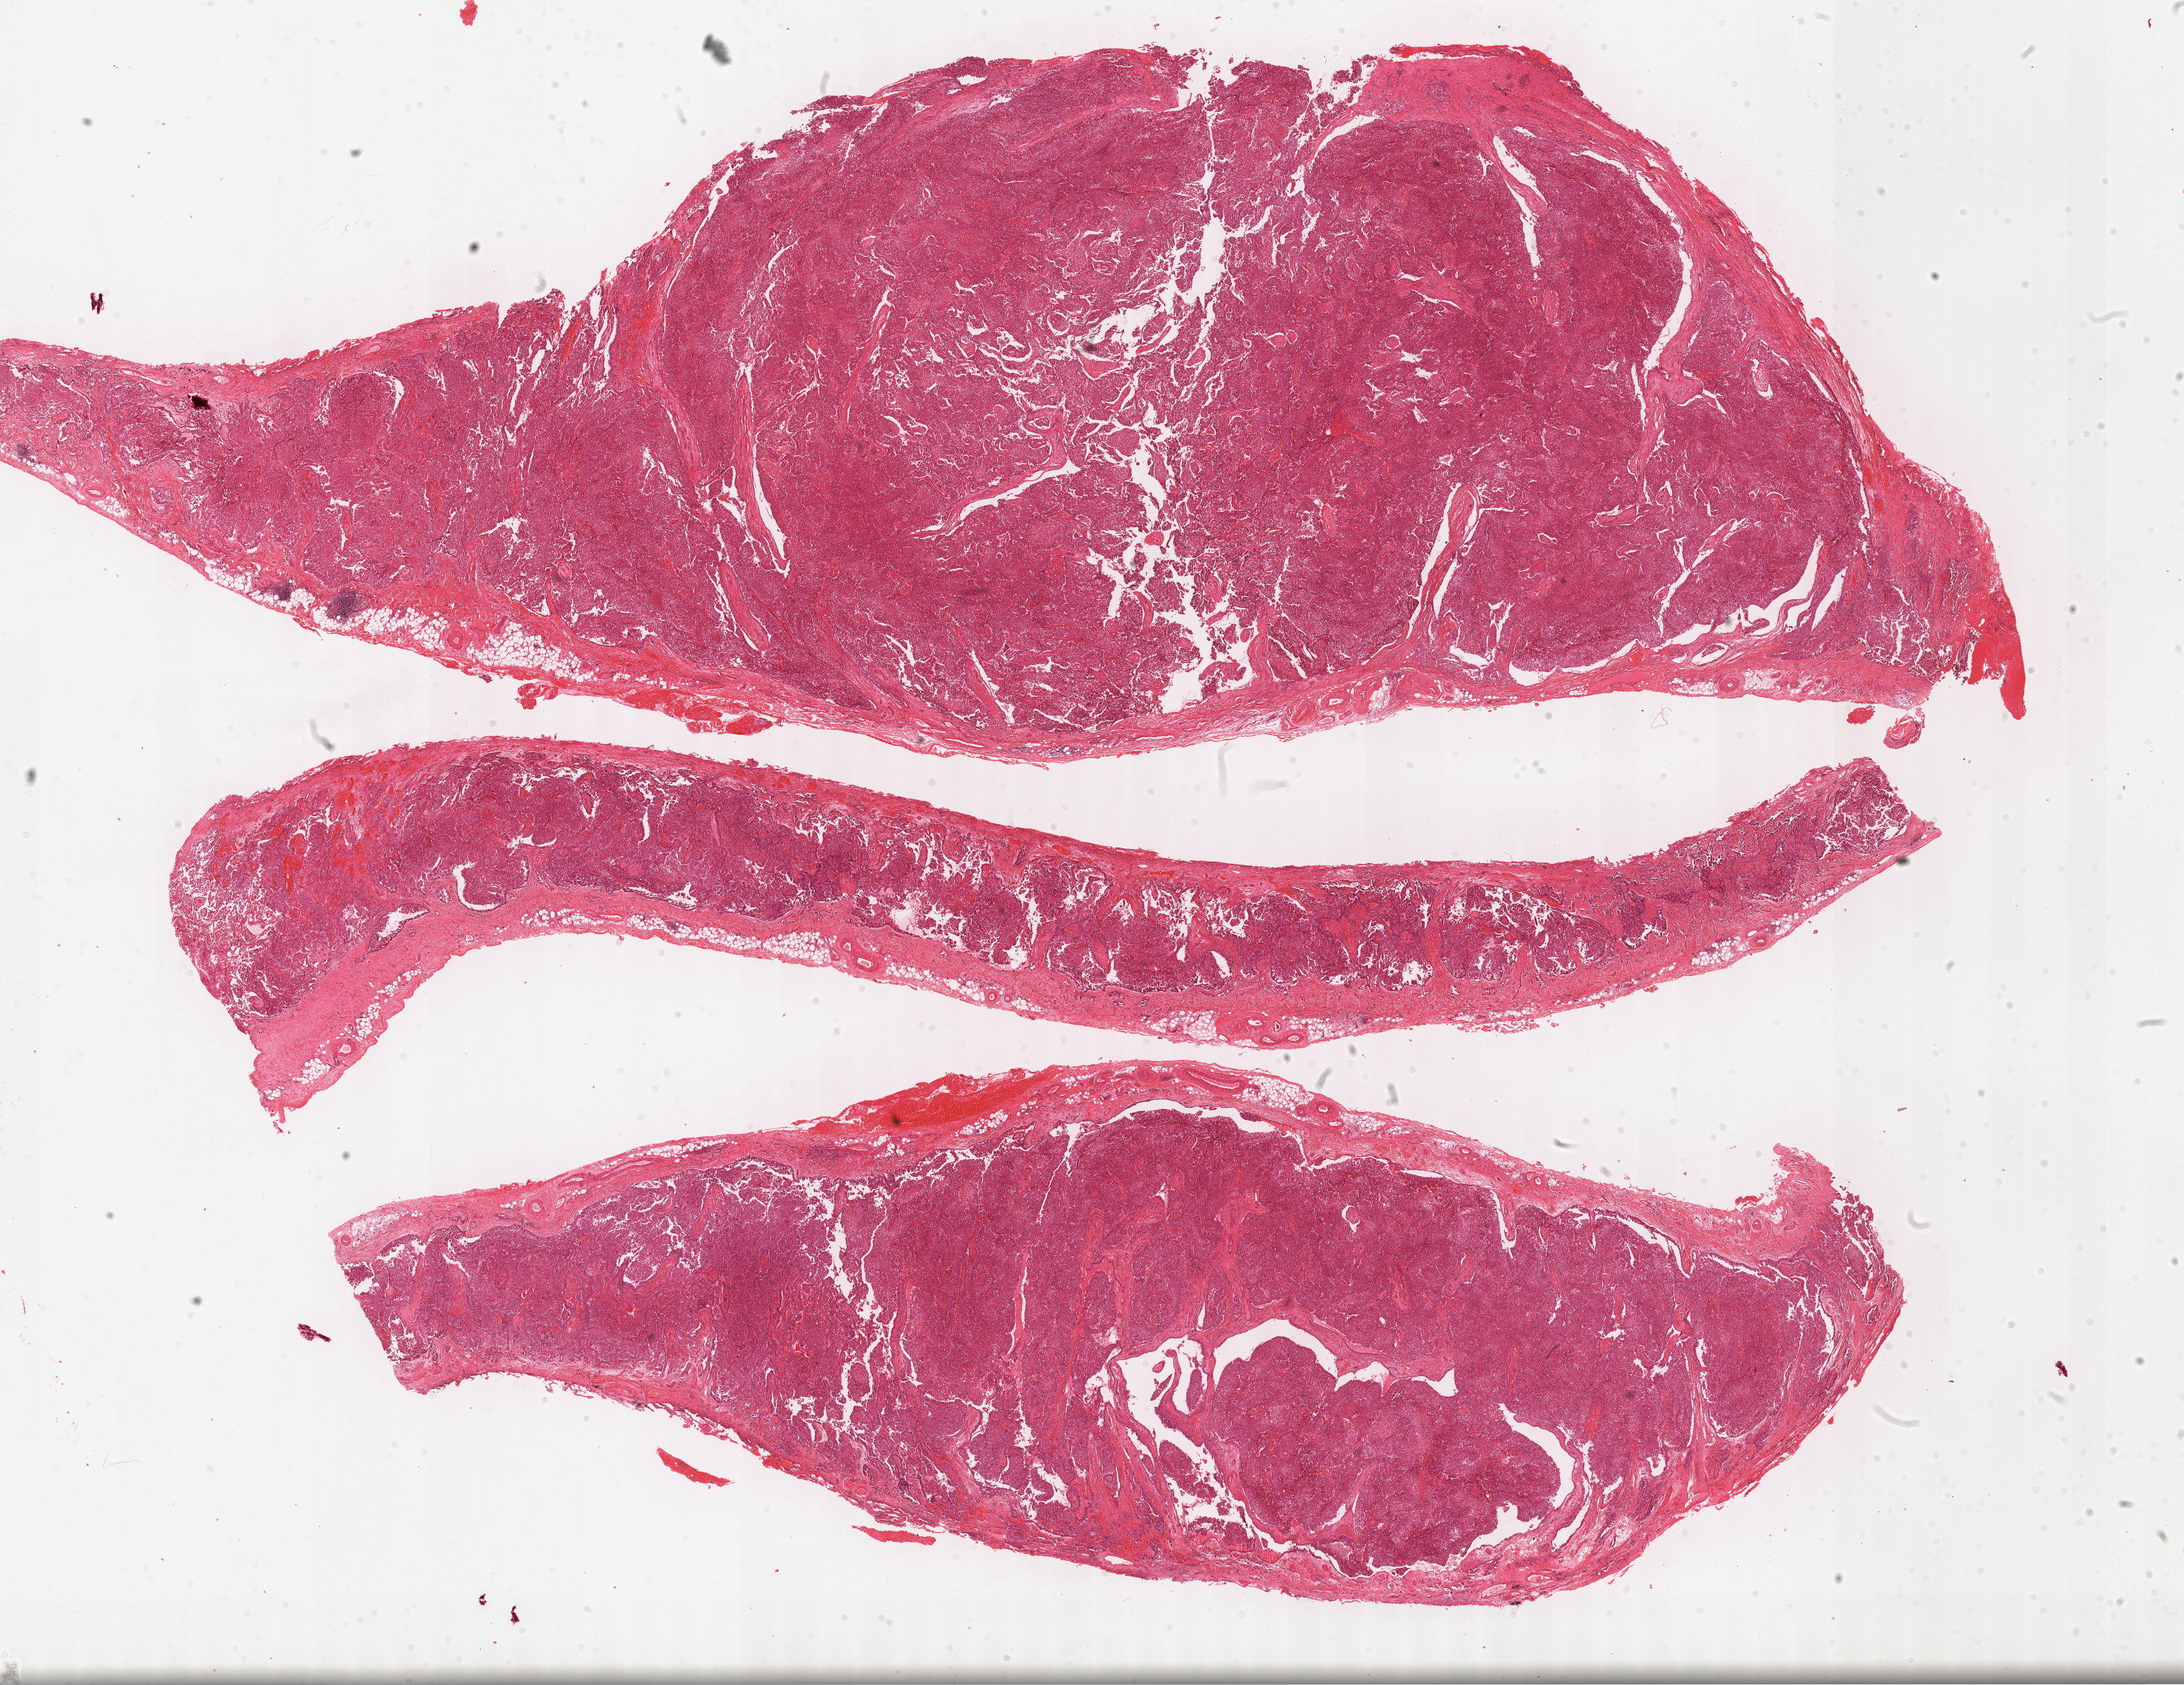
Whole-slide histology image, Hematoxylin and eosin (H&E) stained, a low-resolution overview of the entire scanned area, about 28.2 x 21.7 mm (slide scanned at 40x), formalin-fixed paraffin-embedded (FFPE) diagnostic section, sample: primary tumour, mesothelium. Patient: male, age at initial diagnosis 60 years.
Diagnosis: Epithelioid mesothelioma, malignant (pleura, NOS). AJCC pathologic stage: IV (7th edition). Laterality: right.